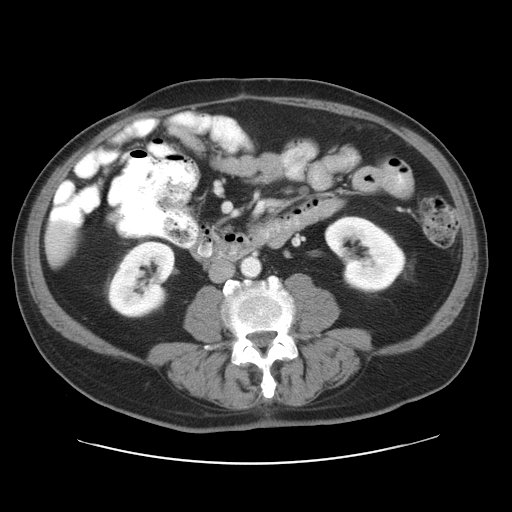
Contrast-enhanced abdominal CT, one axial slice; slice 7 of 28 in the series (ordered by position); reconstruction kernel STANDARD; 120 kVp; intravenous contrast given; soft-tissue window (W 400 / L 40 HU); 7.5 mm slice thickness; 512 × 512 image matrix, field of view 402 × 402 mm. Male patient, age 74 years. Case-level facts recorded for this patient, not image findings: diagnosis: colorectal cancer liver metastases, imaged before liver resection; multiple liver metastases: no; largest metastasis: 5 cm.
Annotated regions visible in this slice (outlined manually by an expert reader):
- liver: bounding box <51,234,70,260> (left, top, right, bottom; pixels)
- planned liver remnant (the part of the liver to remain after resection): <52,233,71,261>